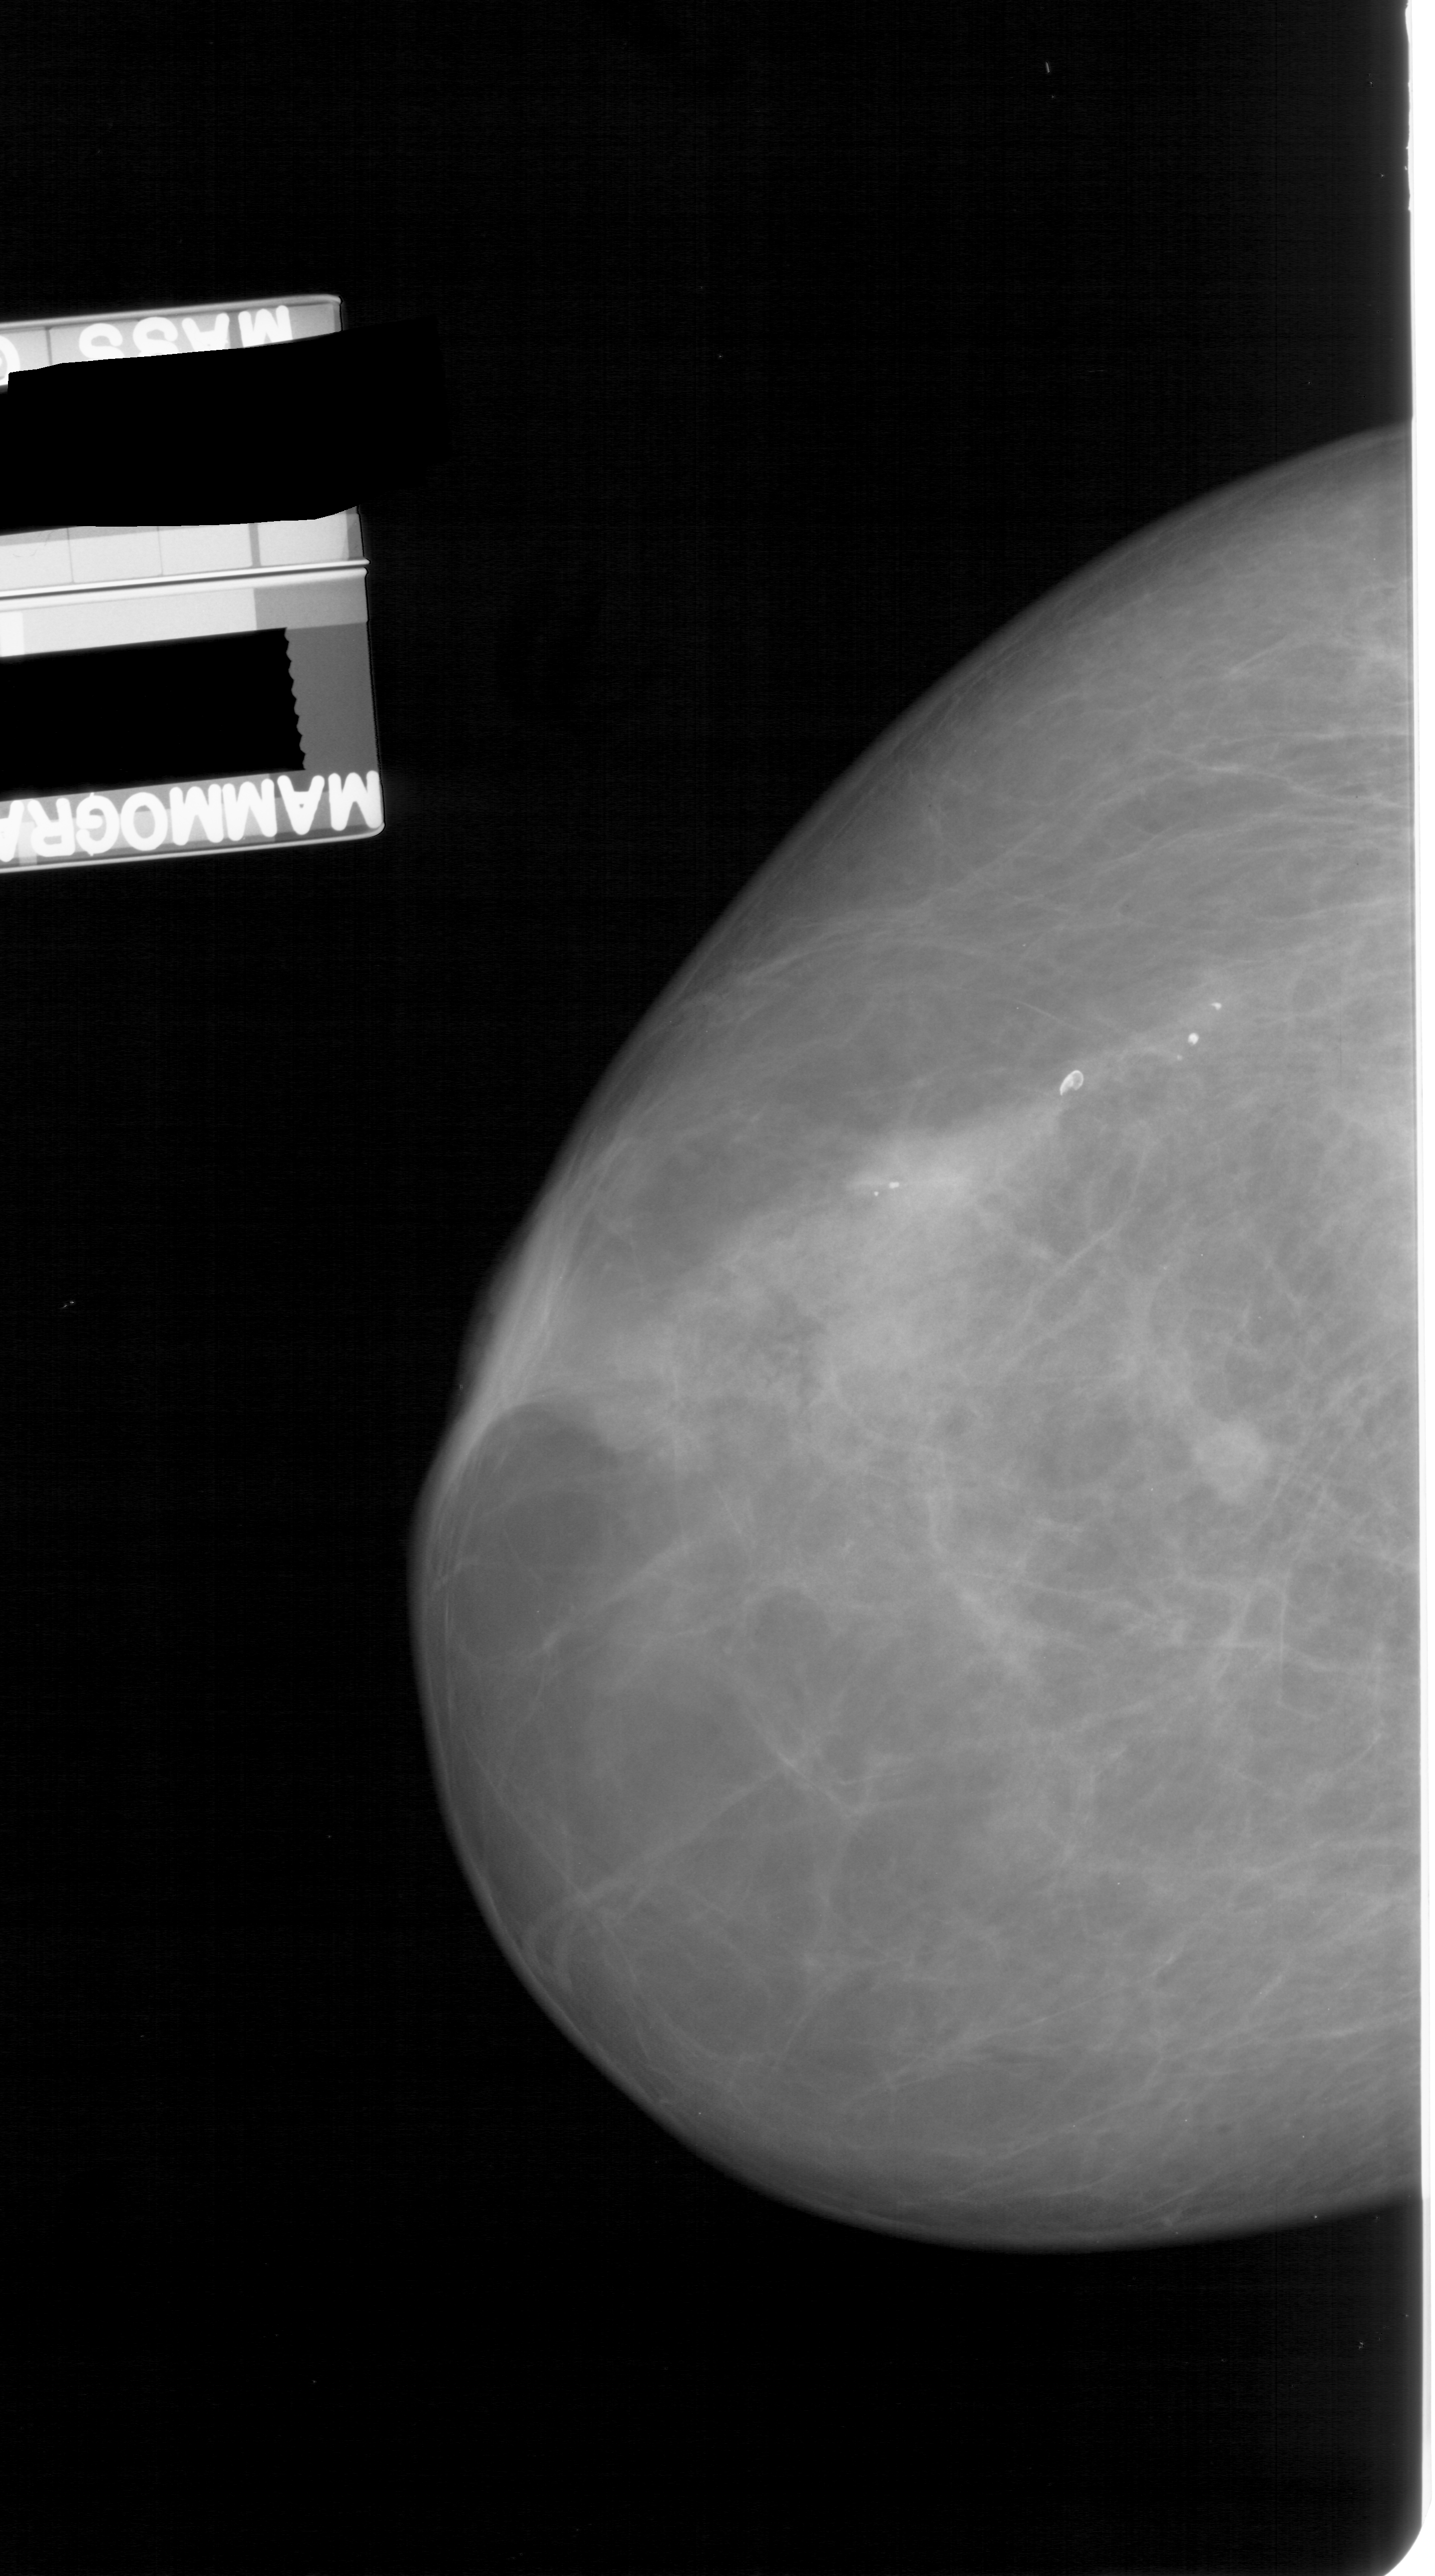
Mammogram (digitized film), left breast, craniocaudal (CC) view, BI-RADS breast density category 4 (scale 1–4).
Abnormality record for this image: mass, shape oval, margins spiculated; BI-RADS assessment category 4; subtlety rating 3 on a 1 (subtle) to 5 (obvious) scale; pathology result (as recorded, not read from the image): malignant.